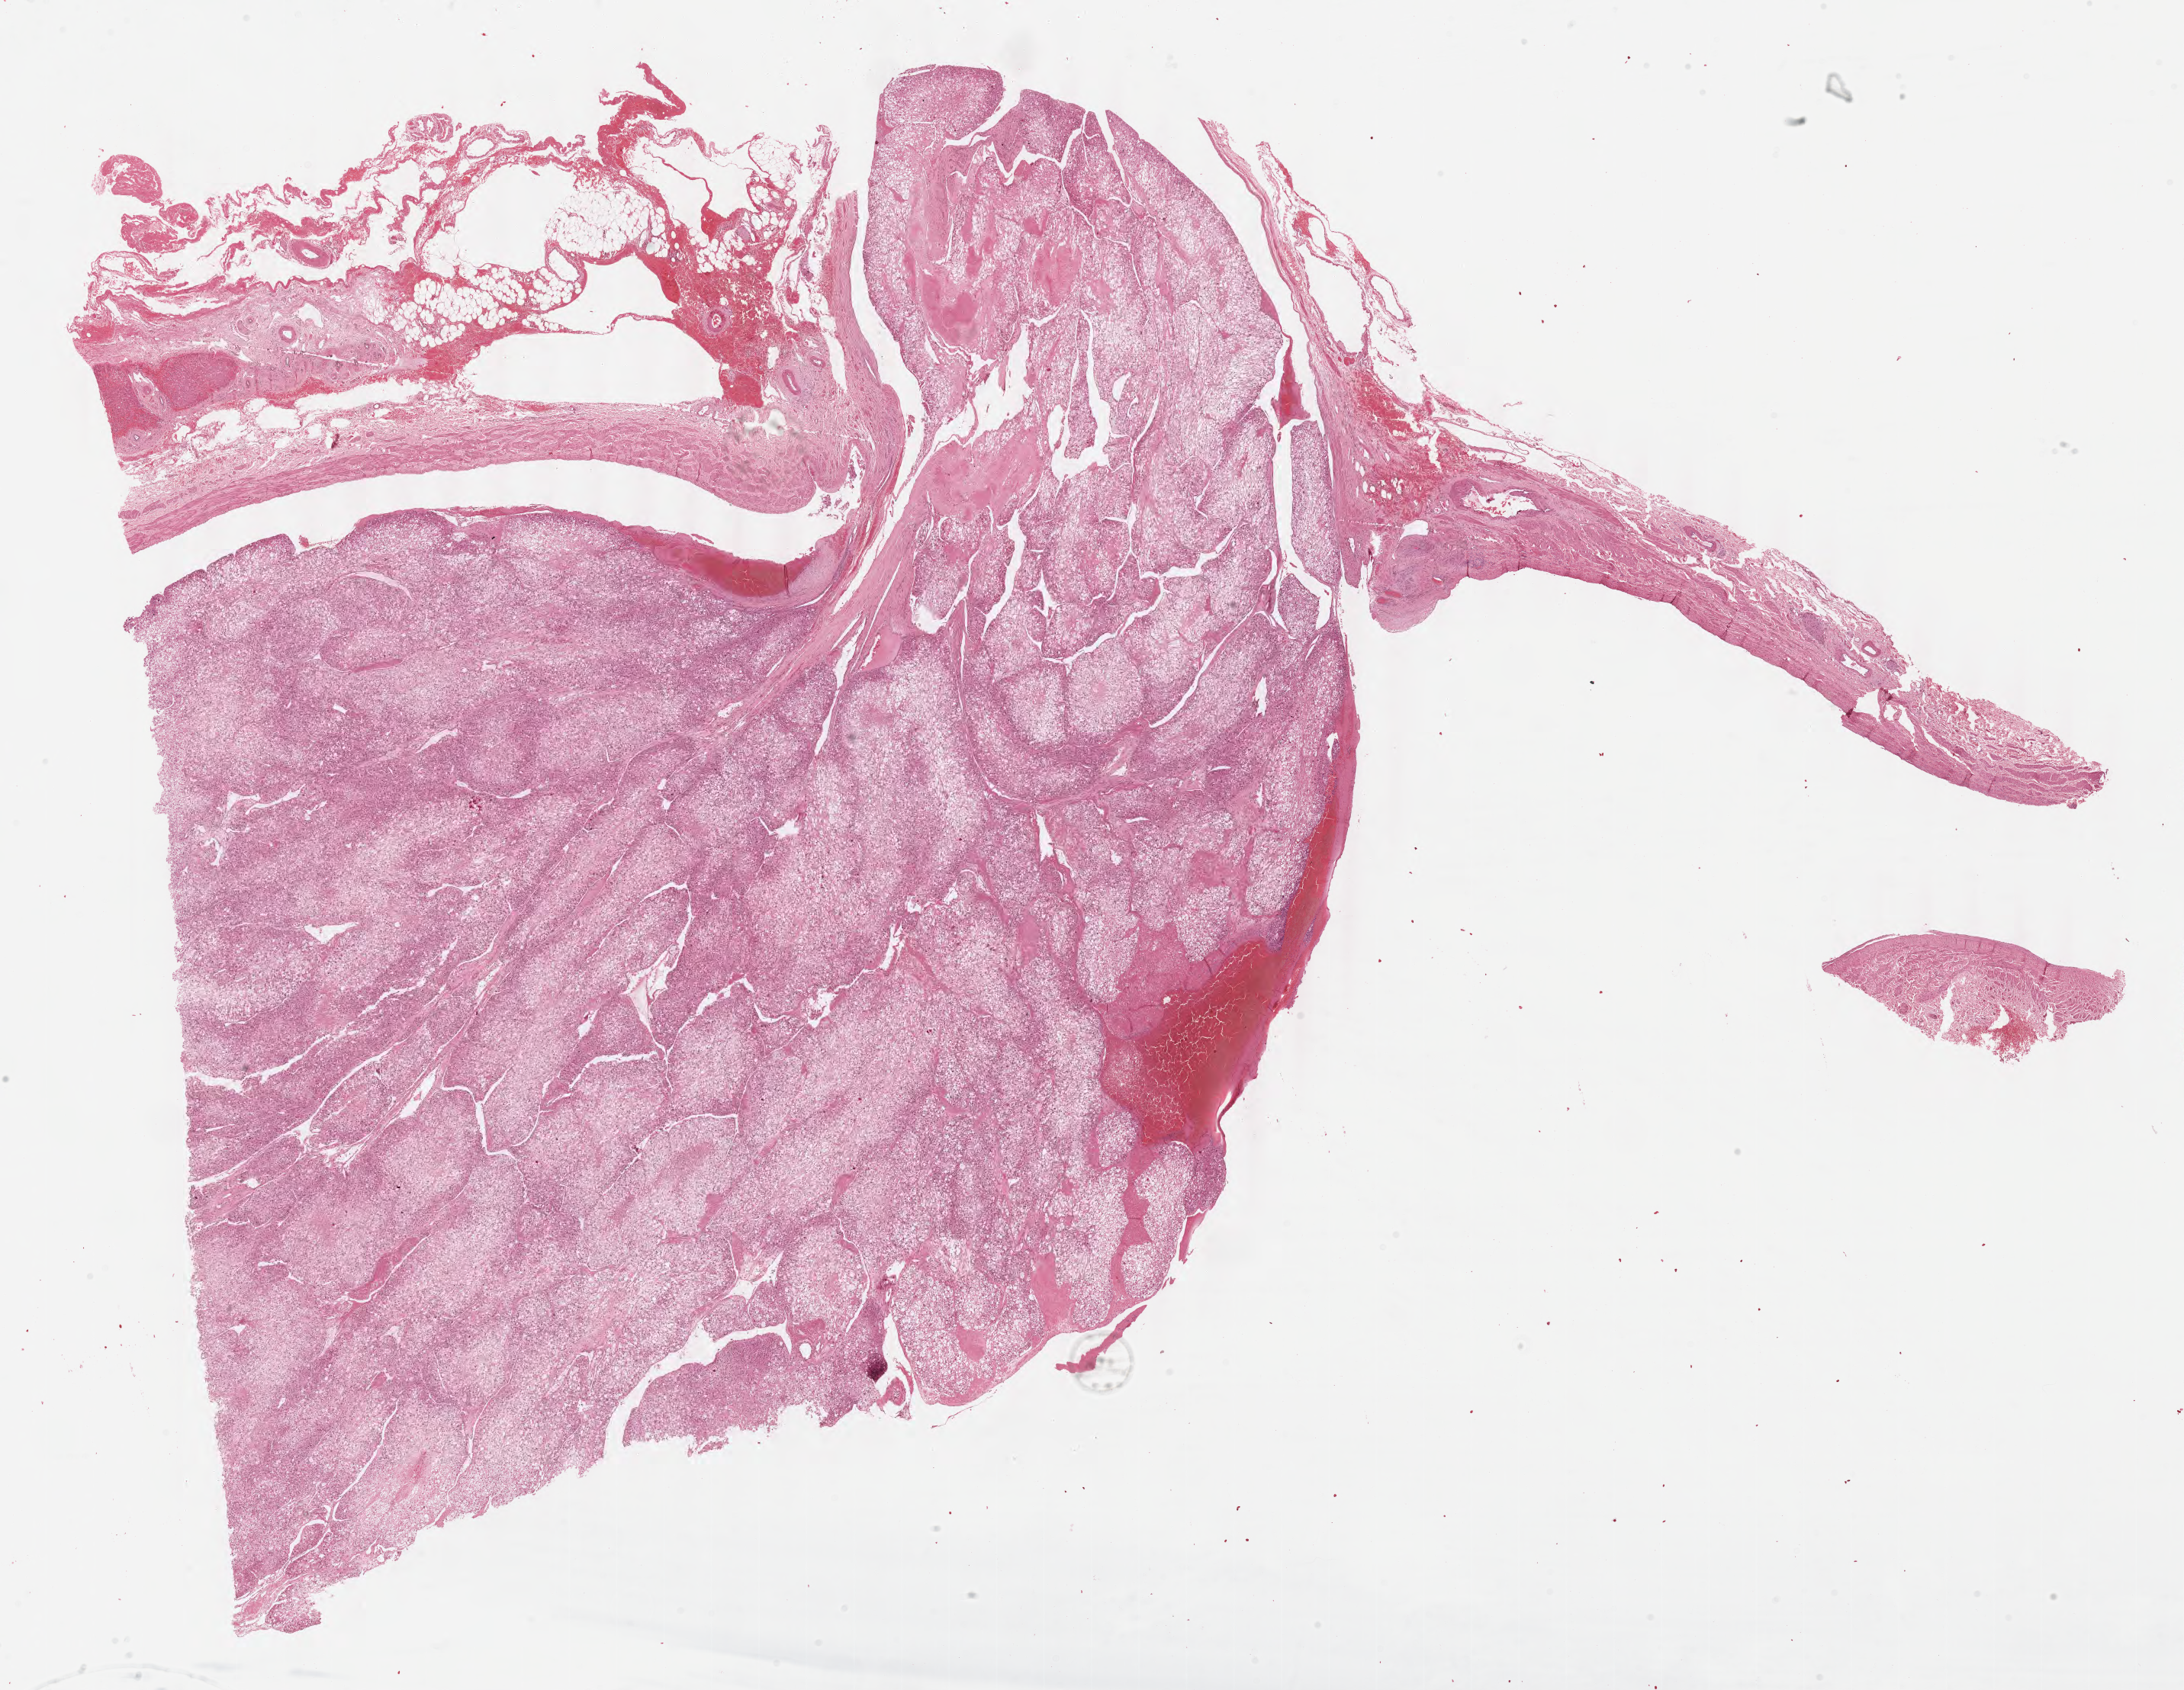
Digitized Hematoxylin and eosin (H&E) stained tissue section (whole slide), a low-resolution overview of the entire scanned area, about 22.6 x 17.5 mm (slide scanned at 40x). Formalin-fixed paraffin-embedded (FFPE) diagnostic section. Adrenal cortex, primary tumour sample. Female patient; age at initial diagnosis 44 years.
Diagnosis: Adrenal cortical carcinoma (cortex of adrenal gland). Lymph nodes positive (case pathology): 0 of 3 examined.